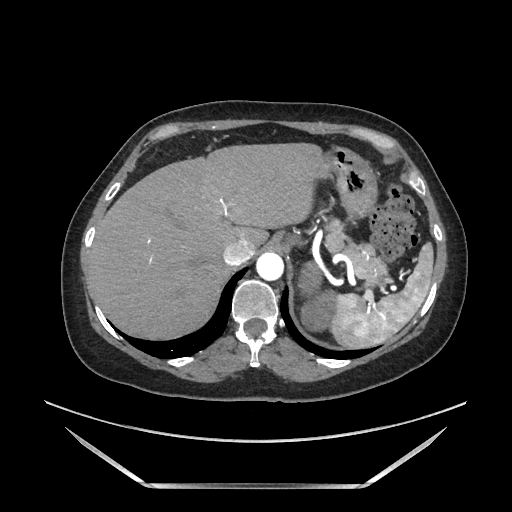
Contrast-enhanced abdominal CT, one axial slice; slice 145 of 205 in the series (ordered by position); soft-tissue window (W 400 / L 40 HU); 512 × 512 image matrix. Female patient. From the clinical record (not read from this slice): diagnosis: adrenocortical carcinoma; tumour side: left adrenal; tumour size at pathology: 12.5 cm; Ki-67 index: 39 %; stage (as recorded): 3.
Structures marked on this image (semi-automatically segmented with operator editing):
- mass: box from (x=299, y=262) to (x=336, y=331) px